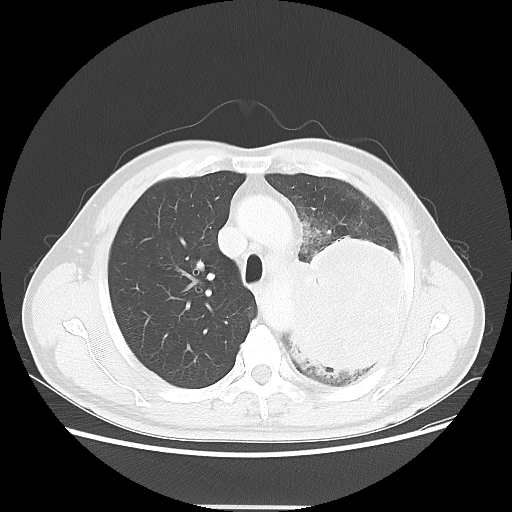
Chest CT, one axial slice; lung window (W 1500 / L -600 HU); 5 mm slice thickness; 512 × 512 image matrix, field of view 391 × 391 mm. Male patient, age 60 years. From the clinical record (not read from this slice): clinical TNM (as recorded): T4 N1 M1a; histopathological grade: G3.
Outlined on this slice (bounding box drawn by a radiologist):
- lung tumour (recorded histology: large cell carcinoma): bounding box (x1, y1, x2, y2) in pixels: (274, 224, 419, 377)